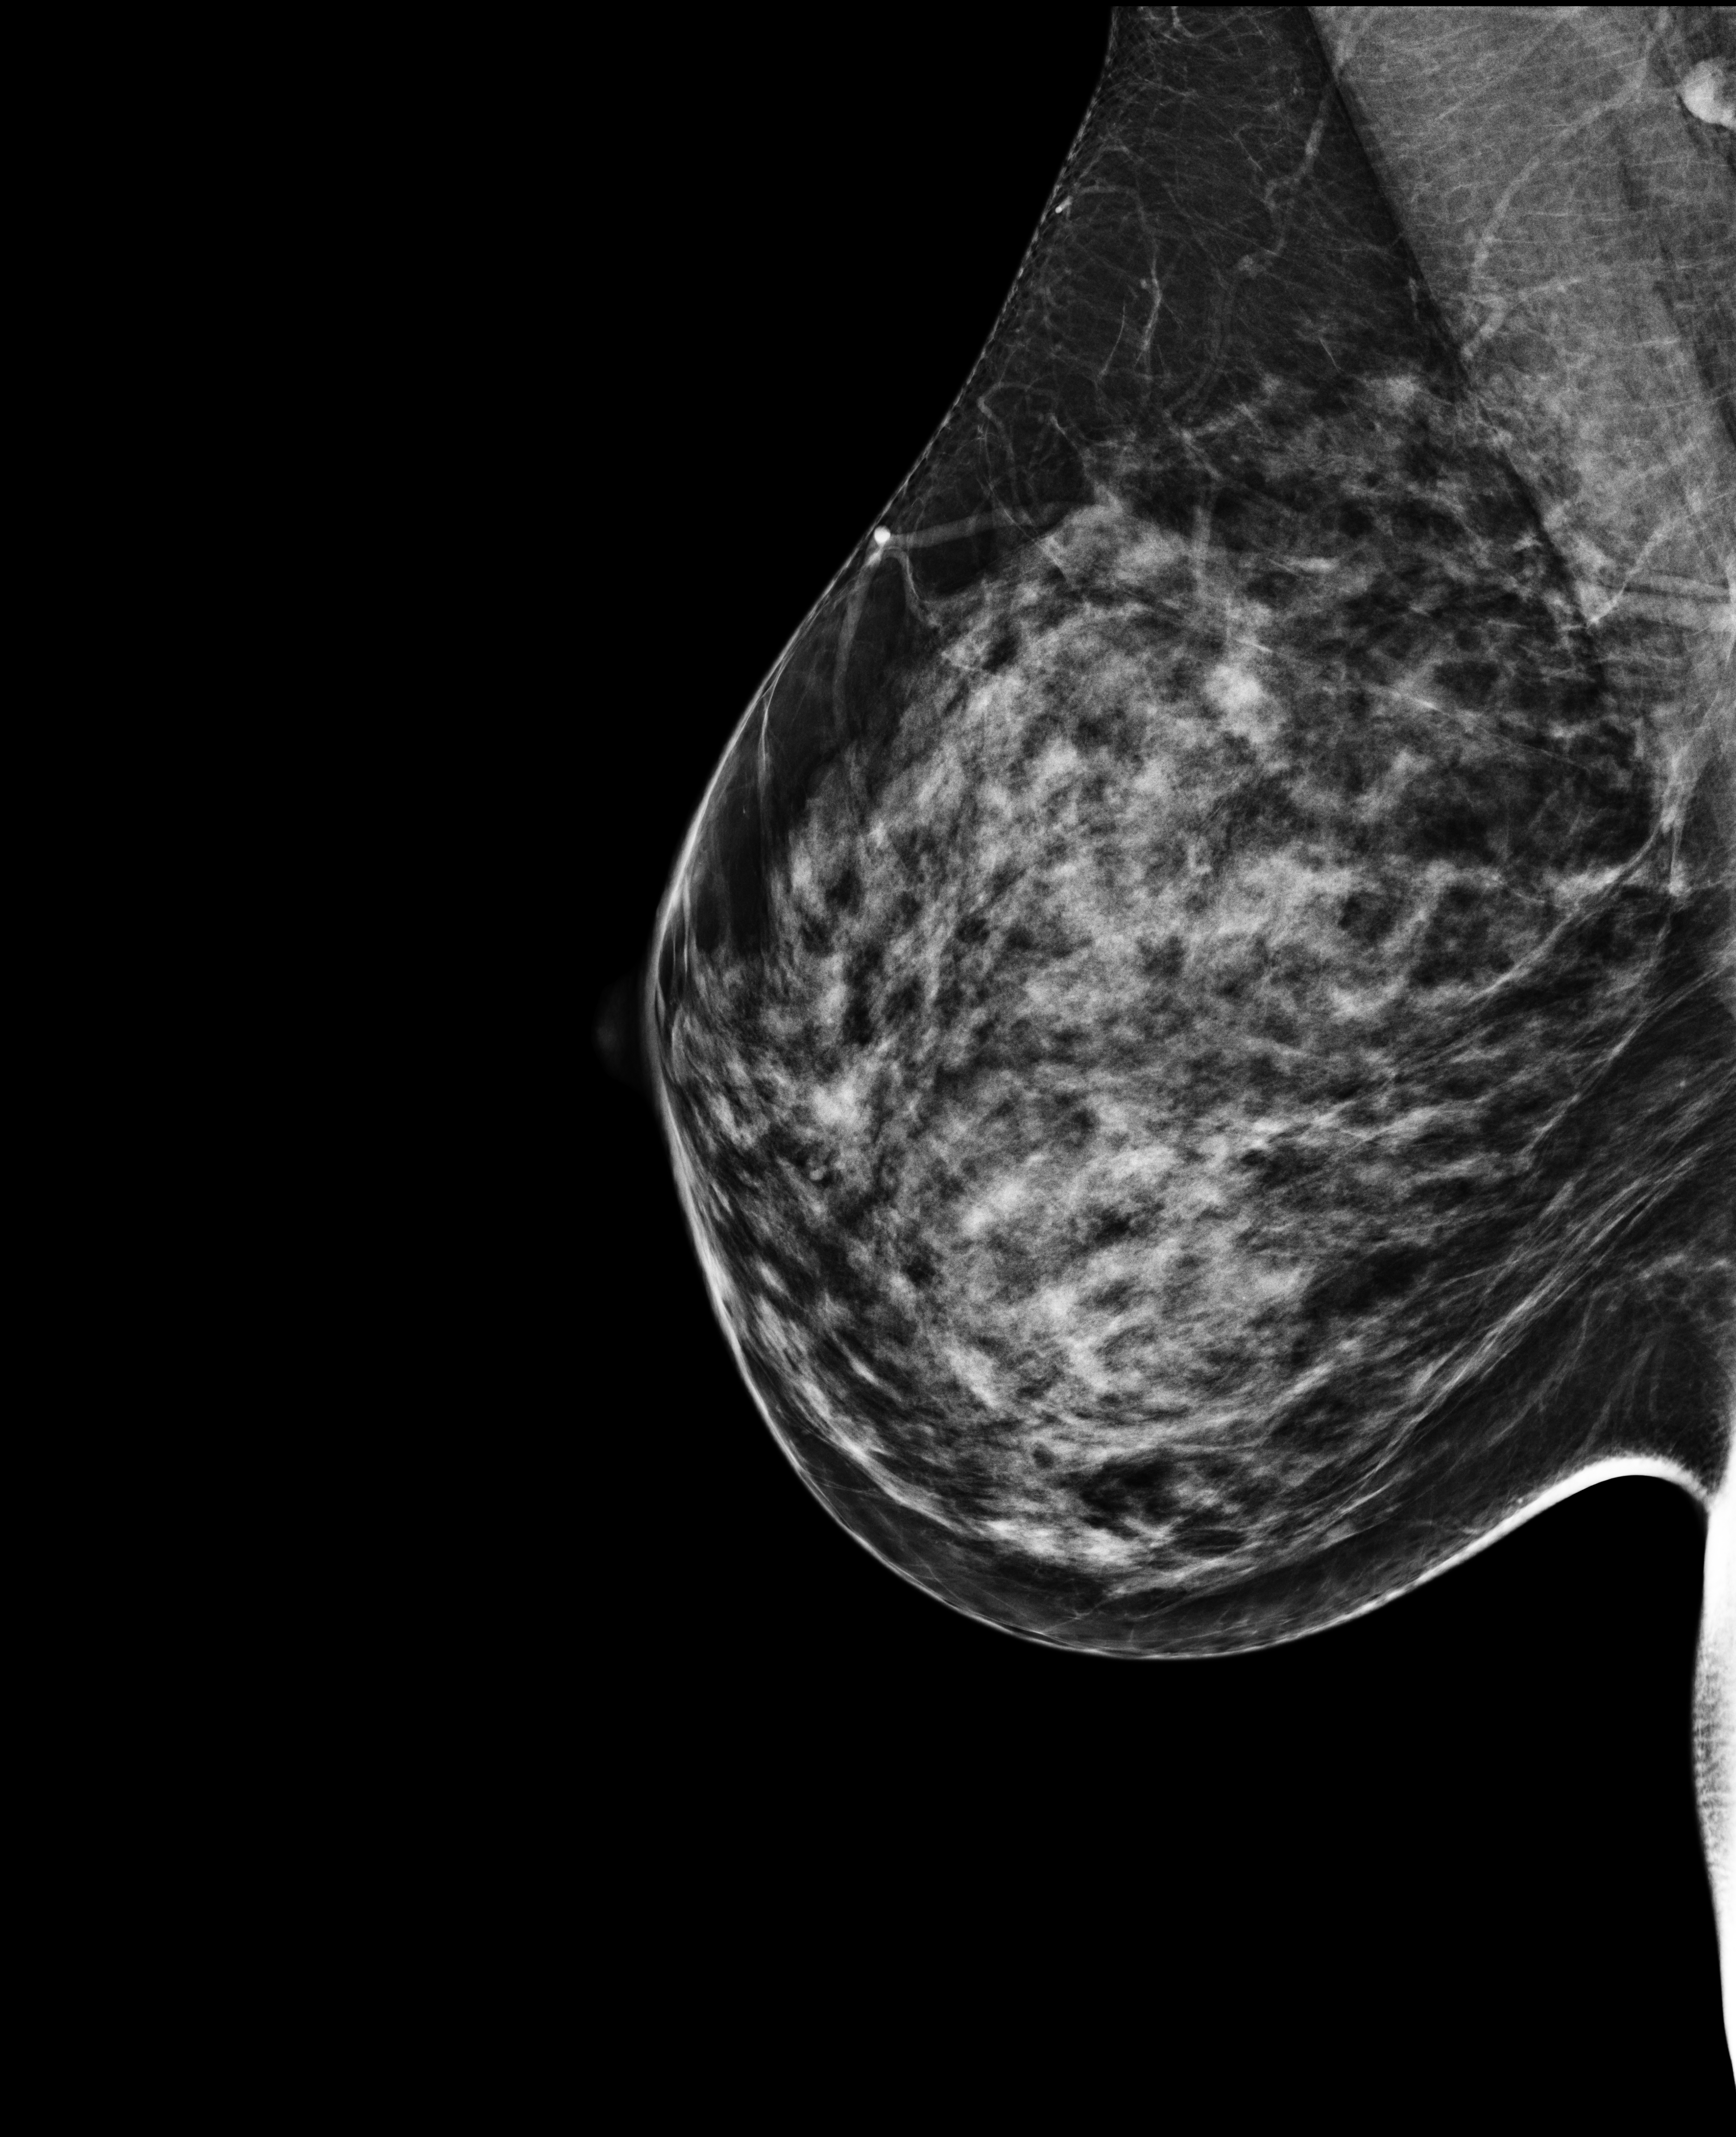
Screening examination; compressed breast thickness 61 mm. Female patient, age 45 years.
Image type: full-field digital mammogram. Breast: right. Projection: MLO view.